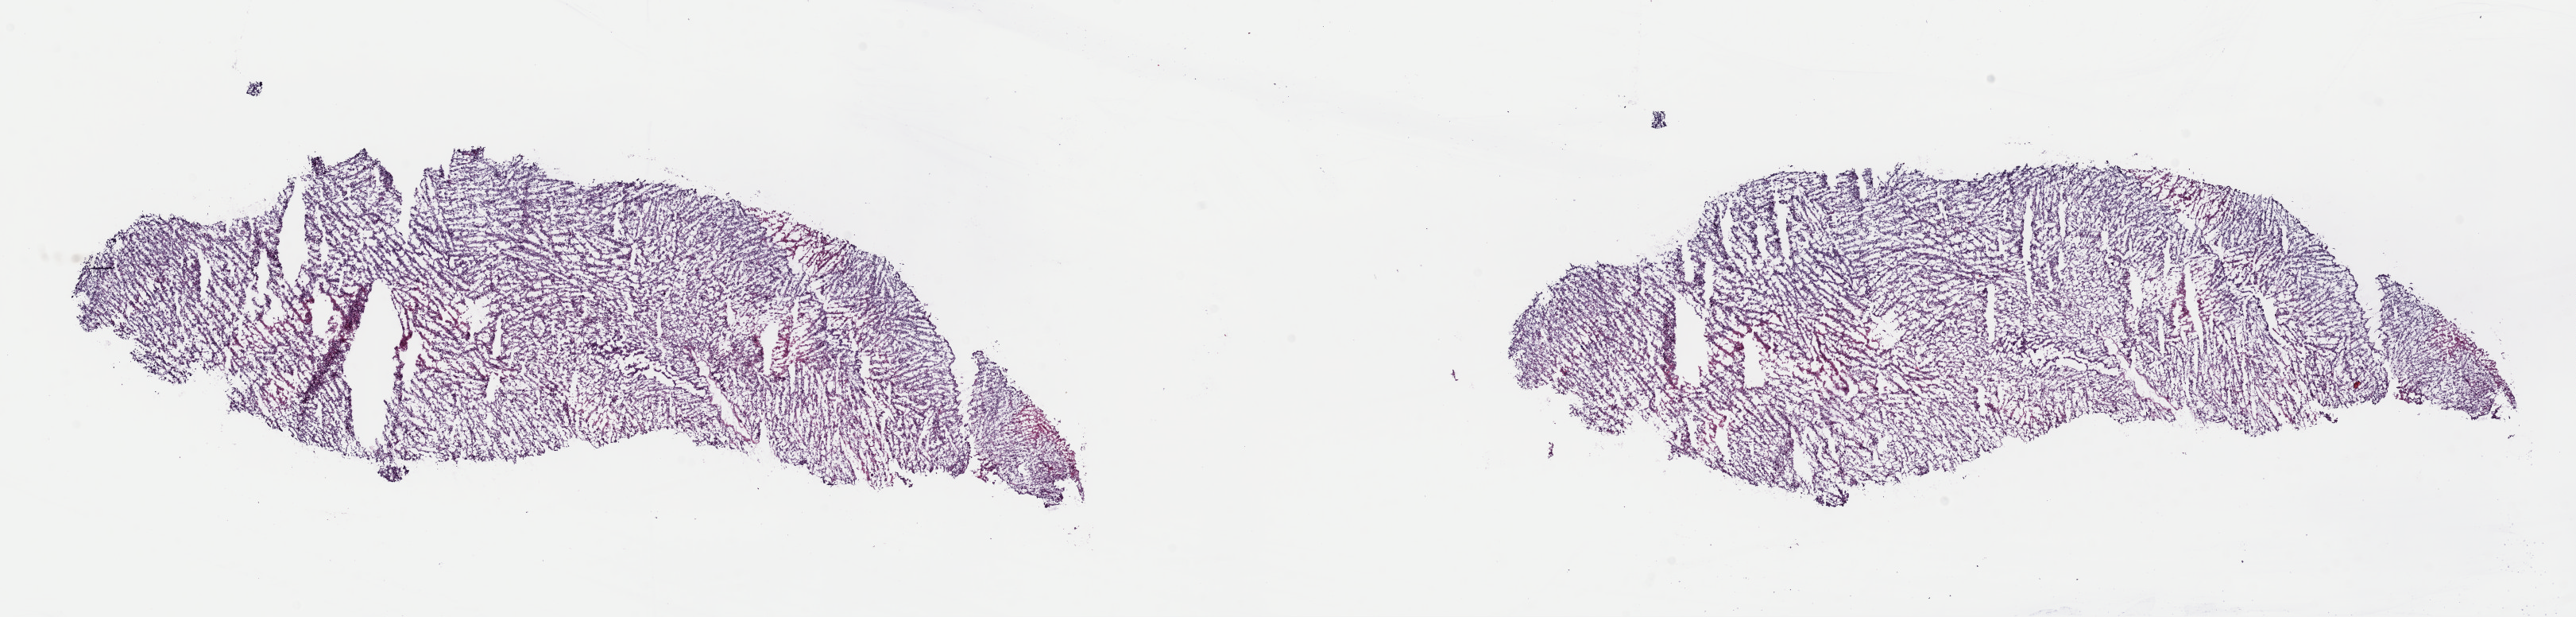
Whole-slide histology image, Hematoxylin and eosin (H&E) stained — shown as a low-resolution overview of the whole scanned area (about 25.6 x 6.1 mm, from a 40x scan), frozen section from the top of the tissue portion, sample: primary tumour, uterus. Female, age 65 years at initial diagnosis. Composition of this section per pathologist review: tumour cells 100%, tumour nuclei 80%, normal cells 0%, stromal cells 0%, necrosis 0%. Inflammatory infiltration, as recorded: lymphocyte infiltration 2%, monocyte infiltration 0%, neutrophil infiltration 0%.
- FIGO stage: IA
- histologic diagnosis: Mullerian mixed tumor